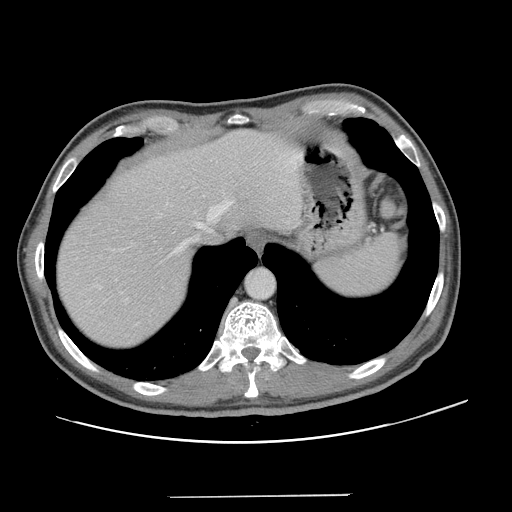
Contrast-enhanced abdominal CT, one axial slice; slice 111 of 131 in the series (ordered by position); 120 kVp; intravenous contrast given; soft-tissue window (W 400 / L 40 HU); 2.5 mm slice thickness; 512 × 512 image matrix, field of view 403 × 403 mm. Male patient, age 60 years. From the clinical record (not read from this slice): diagnosis: colorectal cancer liver metastases, imaged before liver resection; multiple liver metastases: no; largest metastasis: 2.5 cm; disease in both lobes: no.
Annotated regions visible in this slice (expert manual segmentation):
- hepatic veins: bounding box (x1, y1, x2, y2) in pixels: (122, 201, 232, 258)
- liver: (57, 130, 302, 350)
- planned liver remnant (the part of the liver to remain after resection): (57, 131, 302, 341)